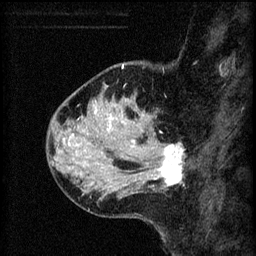
Breast MRI (dynamic contrast-enhanced), one sagittal slice; slice 19 of 60 in the series (ordered by position); 3 images stored at this slice position (order not interpretable as contrast timing); 1.5 T; TE 4.2 ms, TR 8.2 ms; 2 mm slice thickness; 256 × 256 image matrix, field of view 180 × 180 mm. Patient: female, 37 years.
Structures marked on this image (semi-automatically segmented with operator editing):
- analysis volume of interest (the breast-tissue region the enhancement analysis was run in; not a lesion): box from (x=124, y=138) to (x=185, y=195) px
- tumour enhancement mask (voxels above the 70 % enhancement threshold inside the analysis volume of interest): (x=132, y=140)–(x=184, y=187)